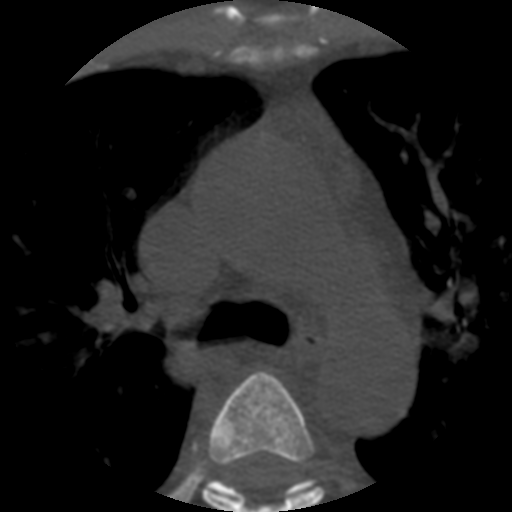
CT including the spine, one axial slice; slice 390 of 508 in the series (ordered by position); 120 kVp; bone window (W 1800 / L 400 HU); 1.25 mm slice thickness; 512 × 512 image matrix. Patient age 57 years. From the clinical record (not read from this slice): primary cancer: prostate.
Outlined on this slice (semi-automatic segmentation, software-assisted and operator-edited):
- T4 vertebra: bounding box <202,371,325,512> (left, top, right, bottom; pixels)
- T5 vertebra: <205,476,316,498>